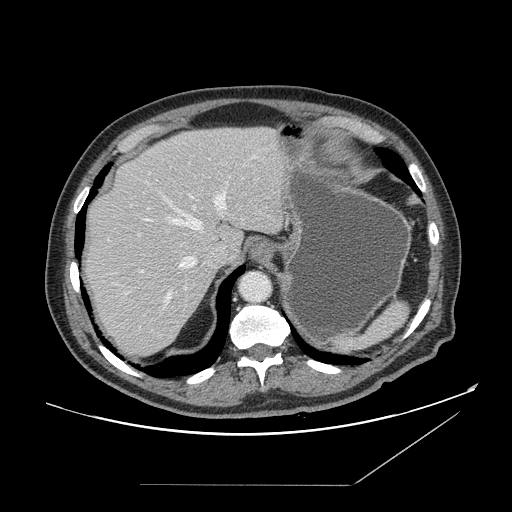
Contrast-enhanced abdominal CT, one axial slice; slice 122 of 166 in the series (ordered by position); soft-tissue window (W 400 / L 40 HU); 2.5 mm slice thickness; 512 × 512 image matrix, field of view 416 × 416 mm. Male patient, age 80 years. Case-level facts recorded for this patient, not image findings: diagnosis: colorectal cancer liver metastases, imaged before liver resection; multiple liver metastases: no.
Outlined on this slice (manually delineated by an expert):
- hepatic veins: bounding box <126,190,226,307> (left, top, right, bottom; pixels)
- liver: <83,127,287,356>
- planned liver remnant (the part of the liver to remain after resection): <86,127,287,255>
- portal vein (with intrahepatic branches): <140,206,196,273>